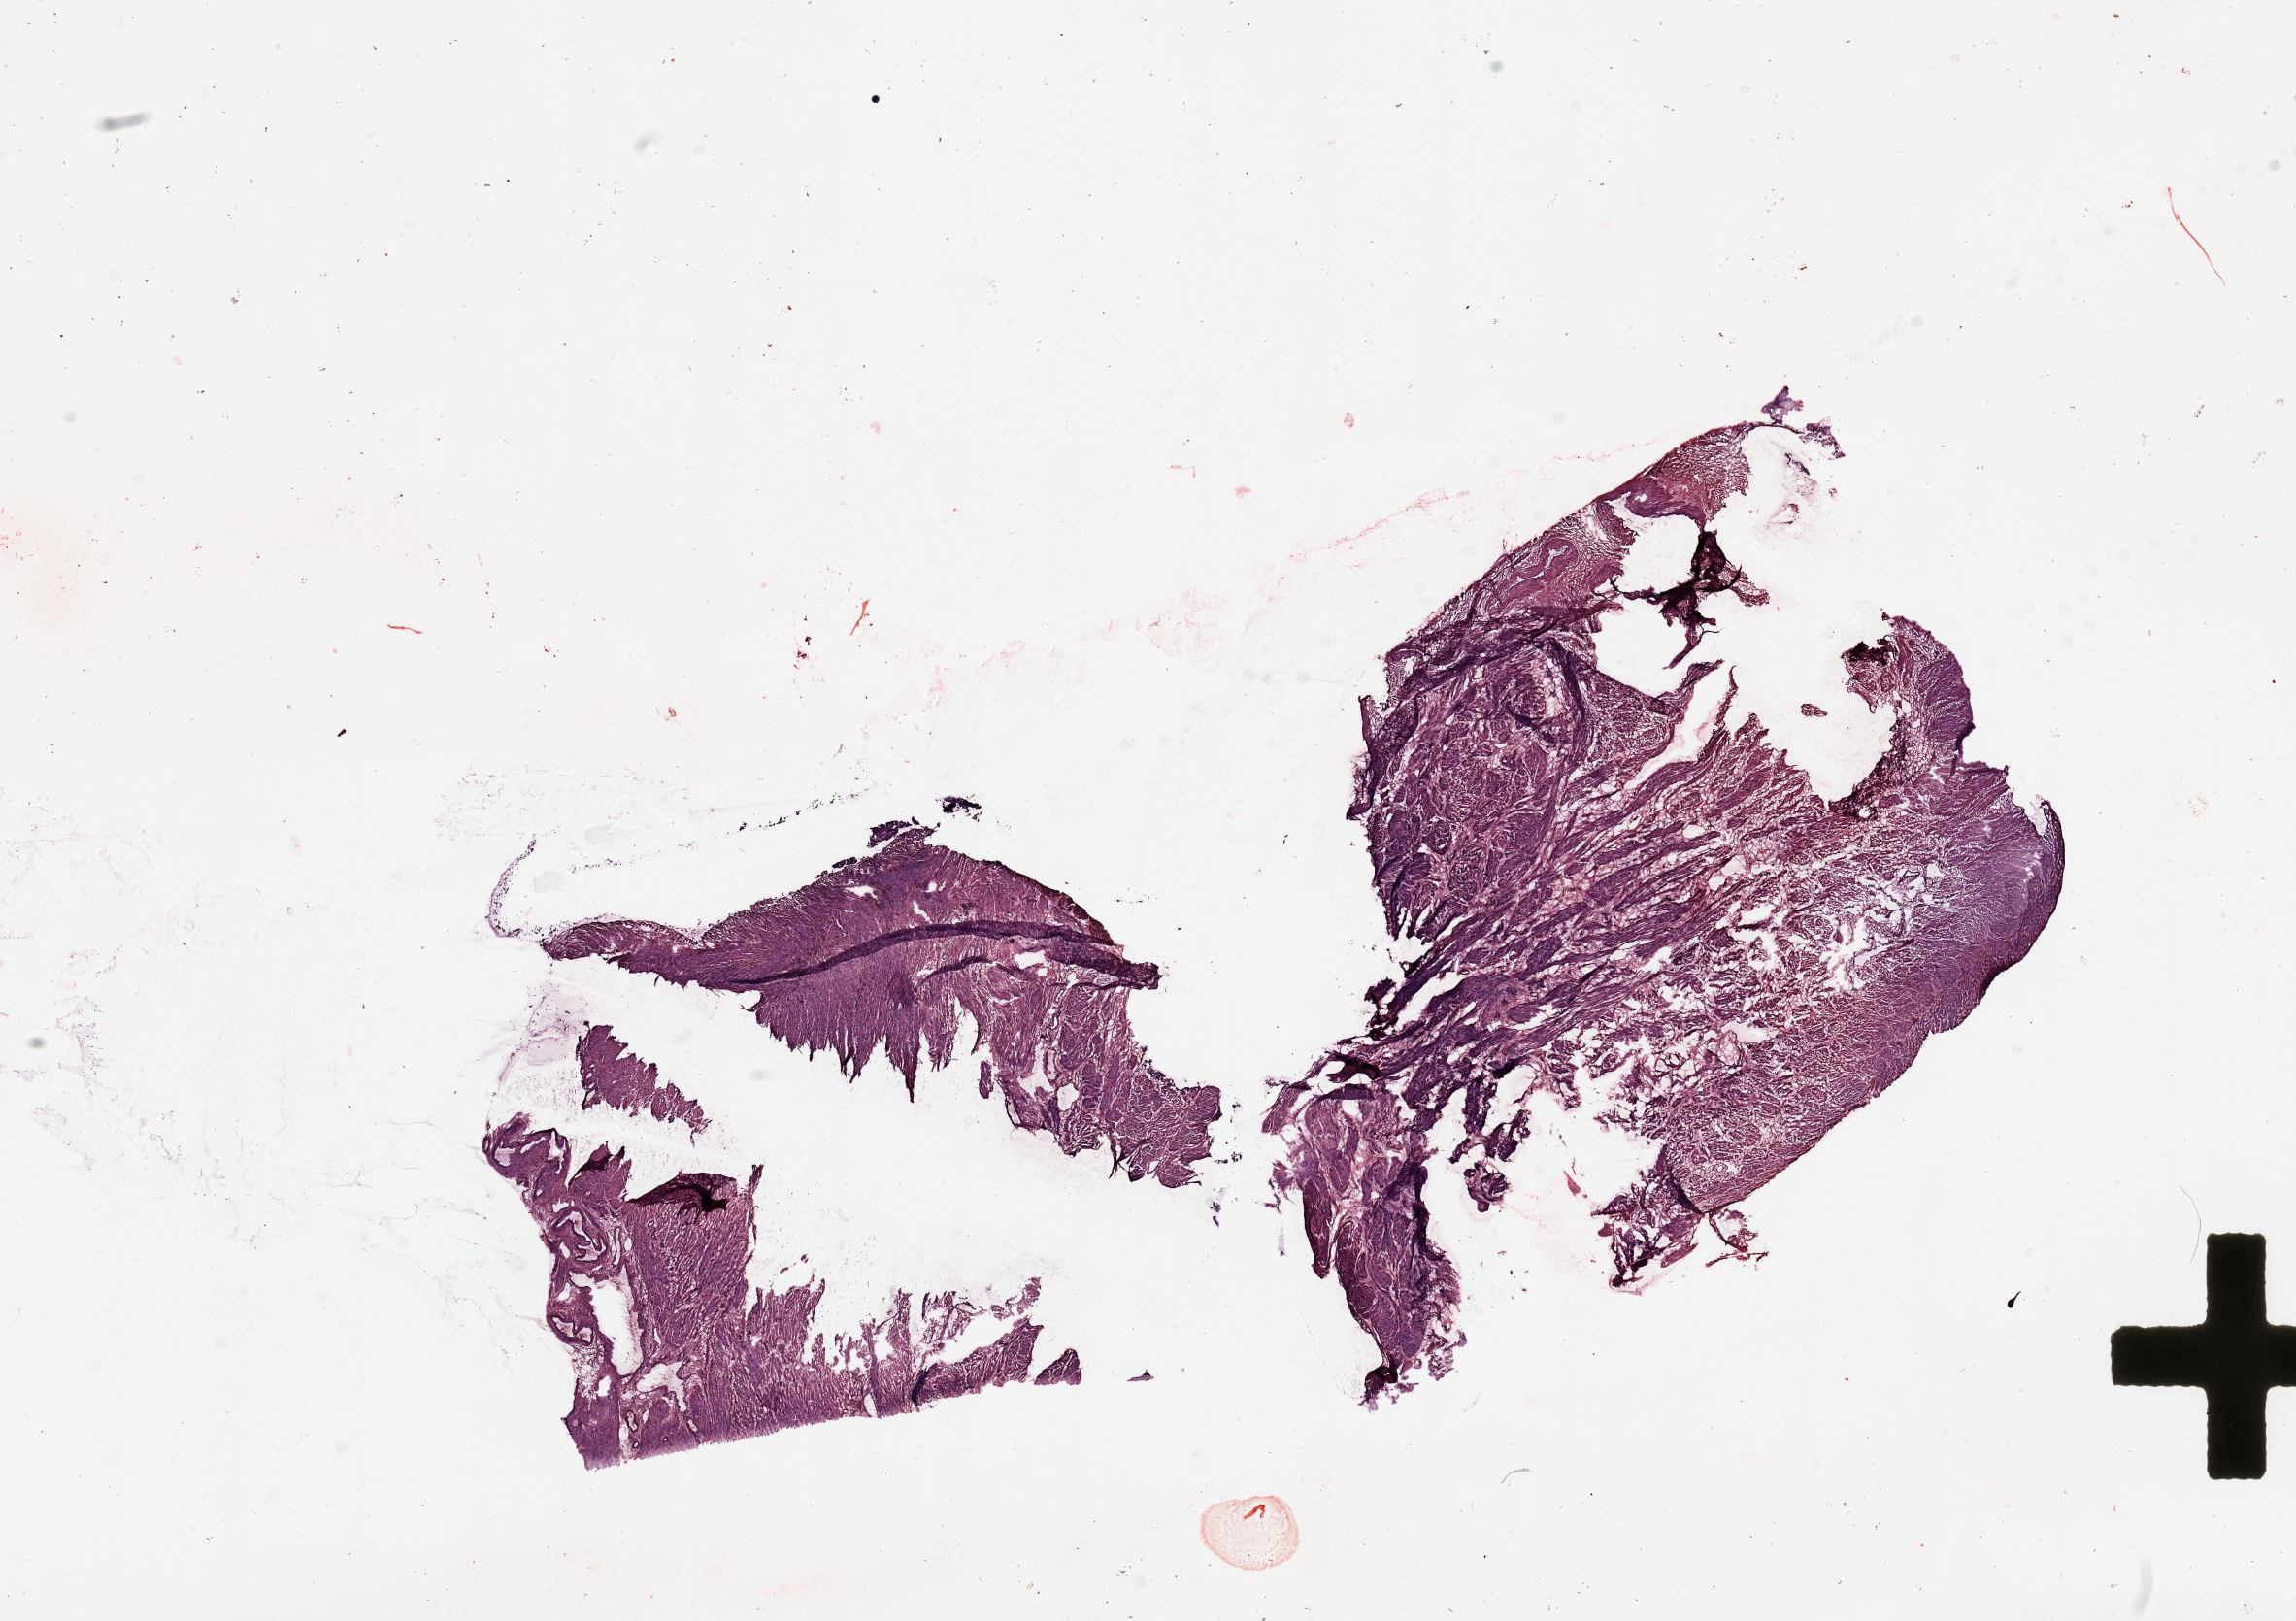
H&E whole-slide image — whole scanned area (about 18.7 x 13.2 mm, from a 20x scan) shown as a low-resolution overview. Uterus, normal (non-tumour) tissue. Patient: female, age 45 years.
* this section: normal (non-tumour) tissue from the same patient
* patient diagnosis: Endometrioid adenocarcinoma, NOS